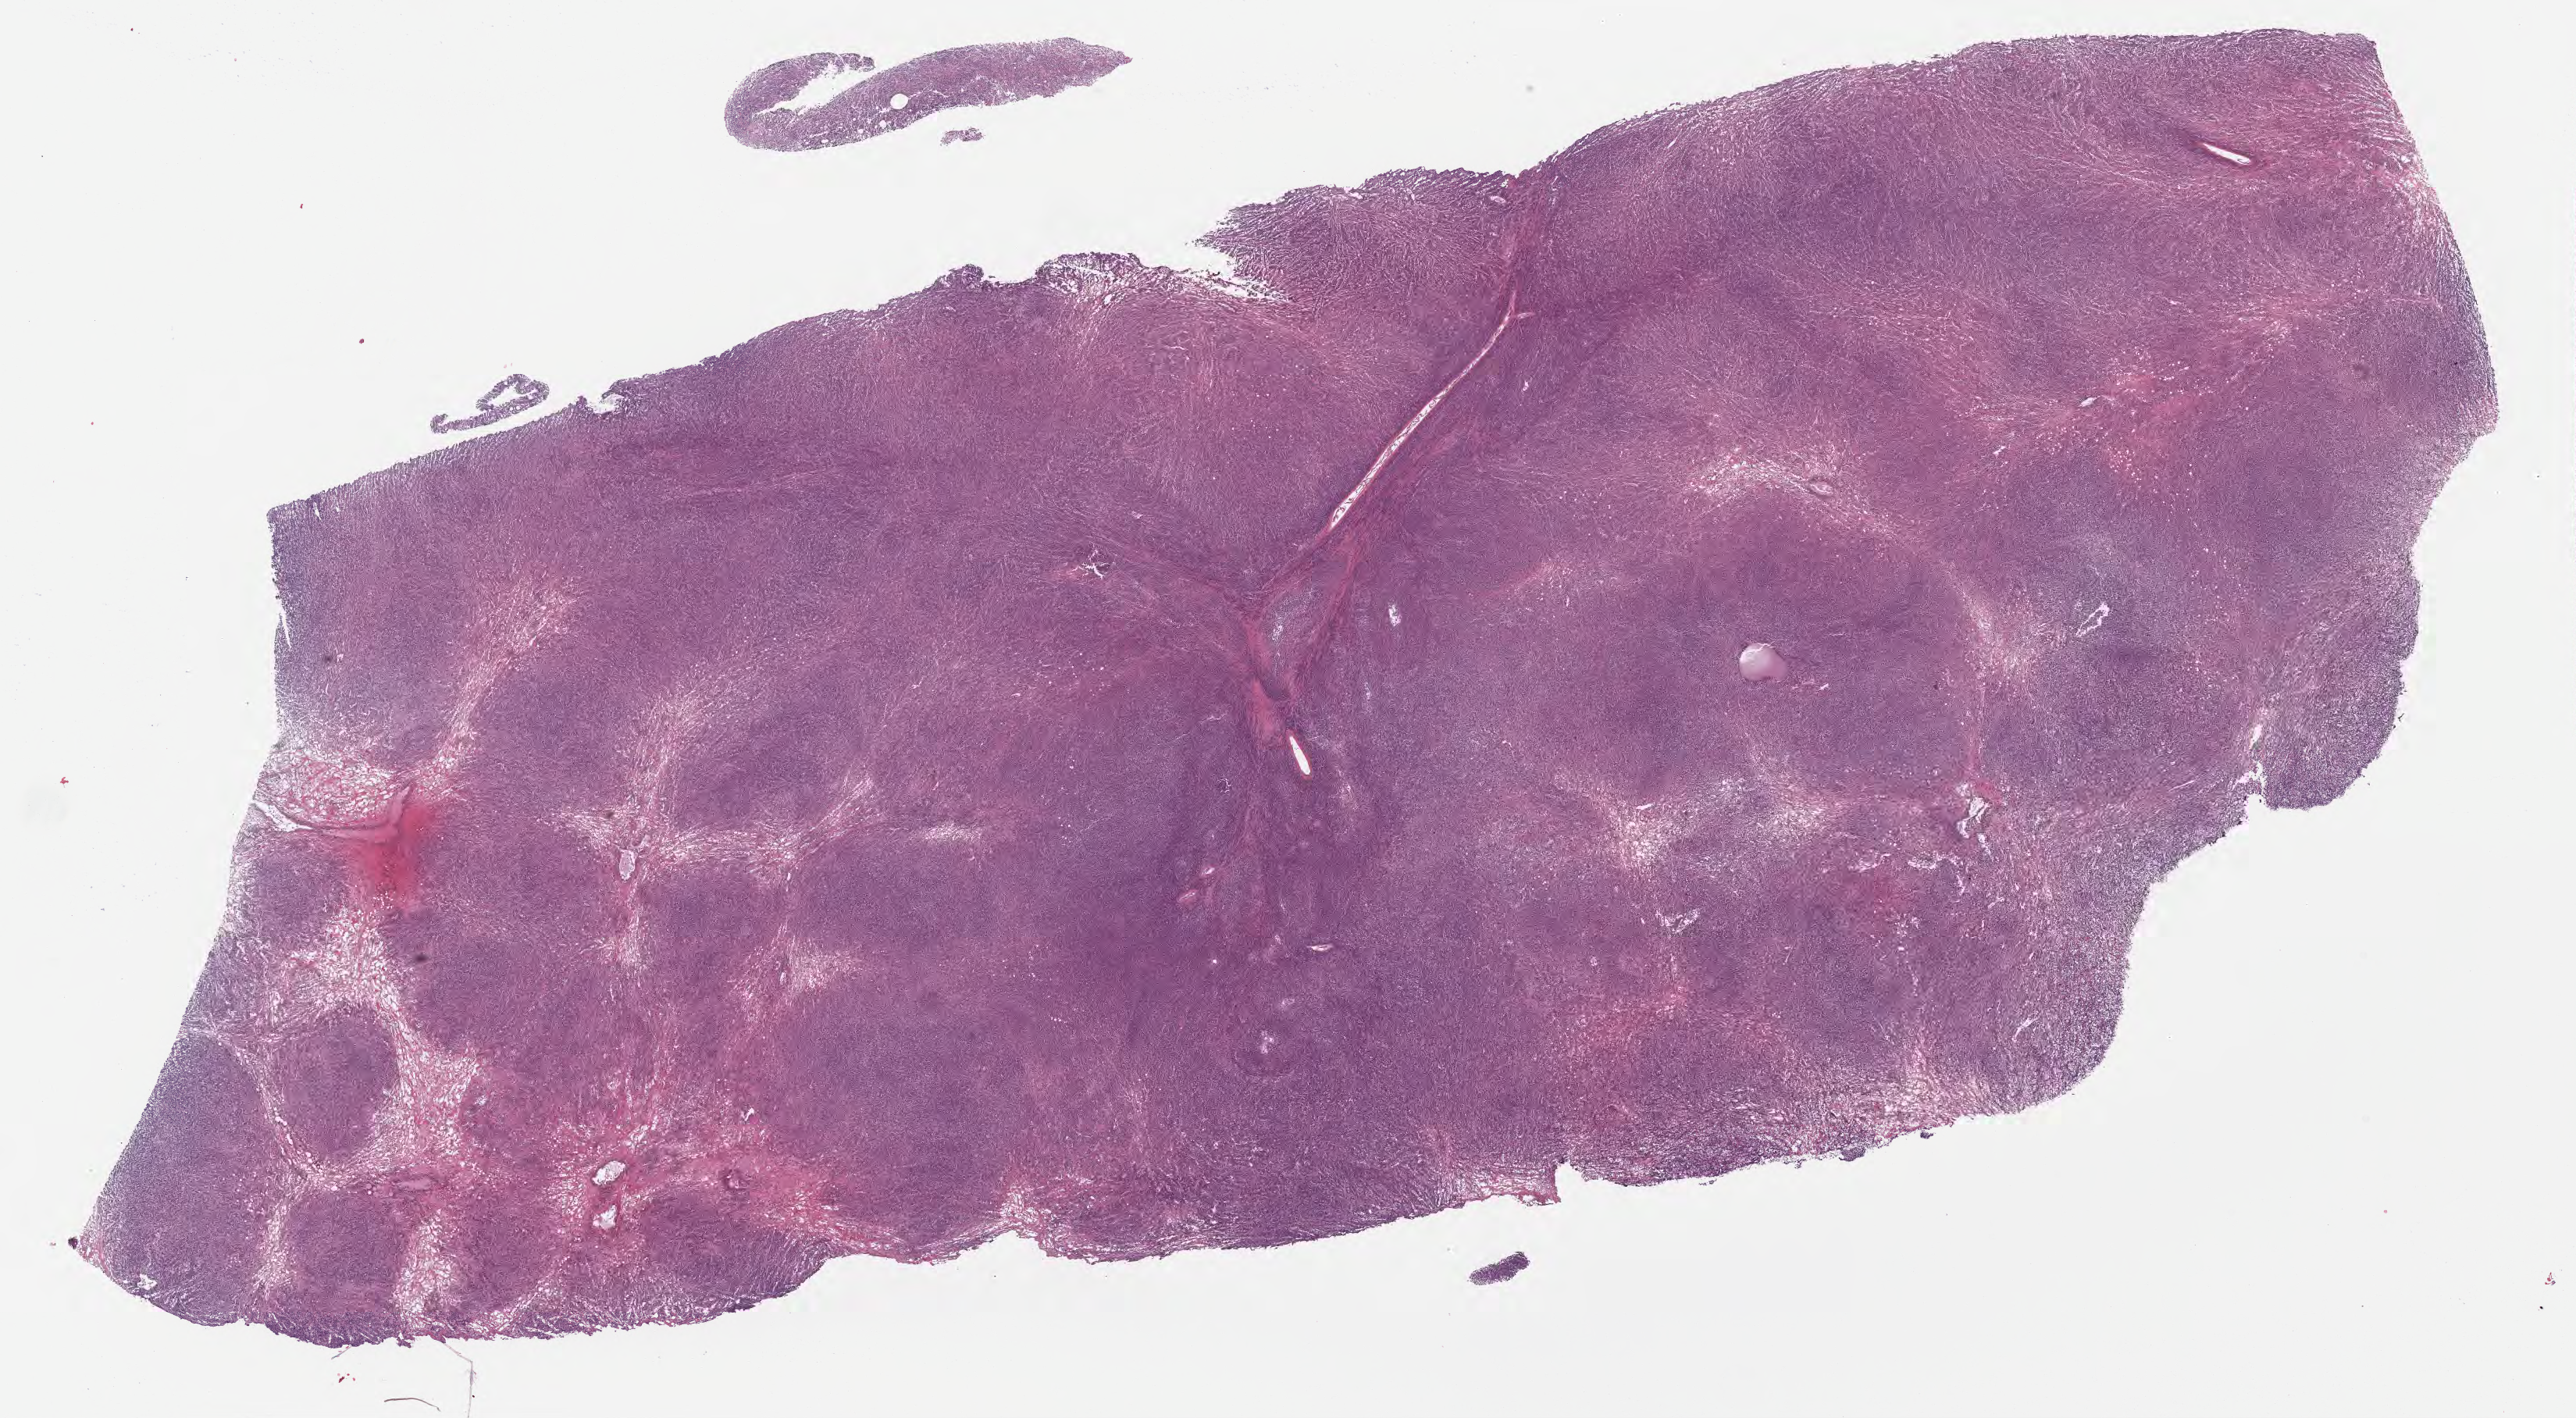
H&E whole-slide image — low-resolution overview of the scanned area, about 26.7 x 14.7 mm. Tumor tissue. Male patient, 39 years old.
Diagnosis: Diffuse large B-cell lymphoma, NOS.